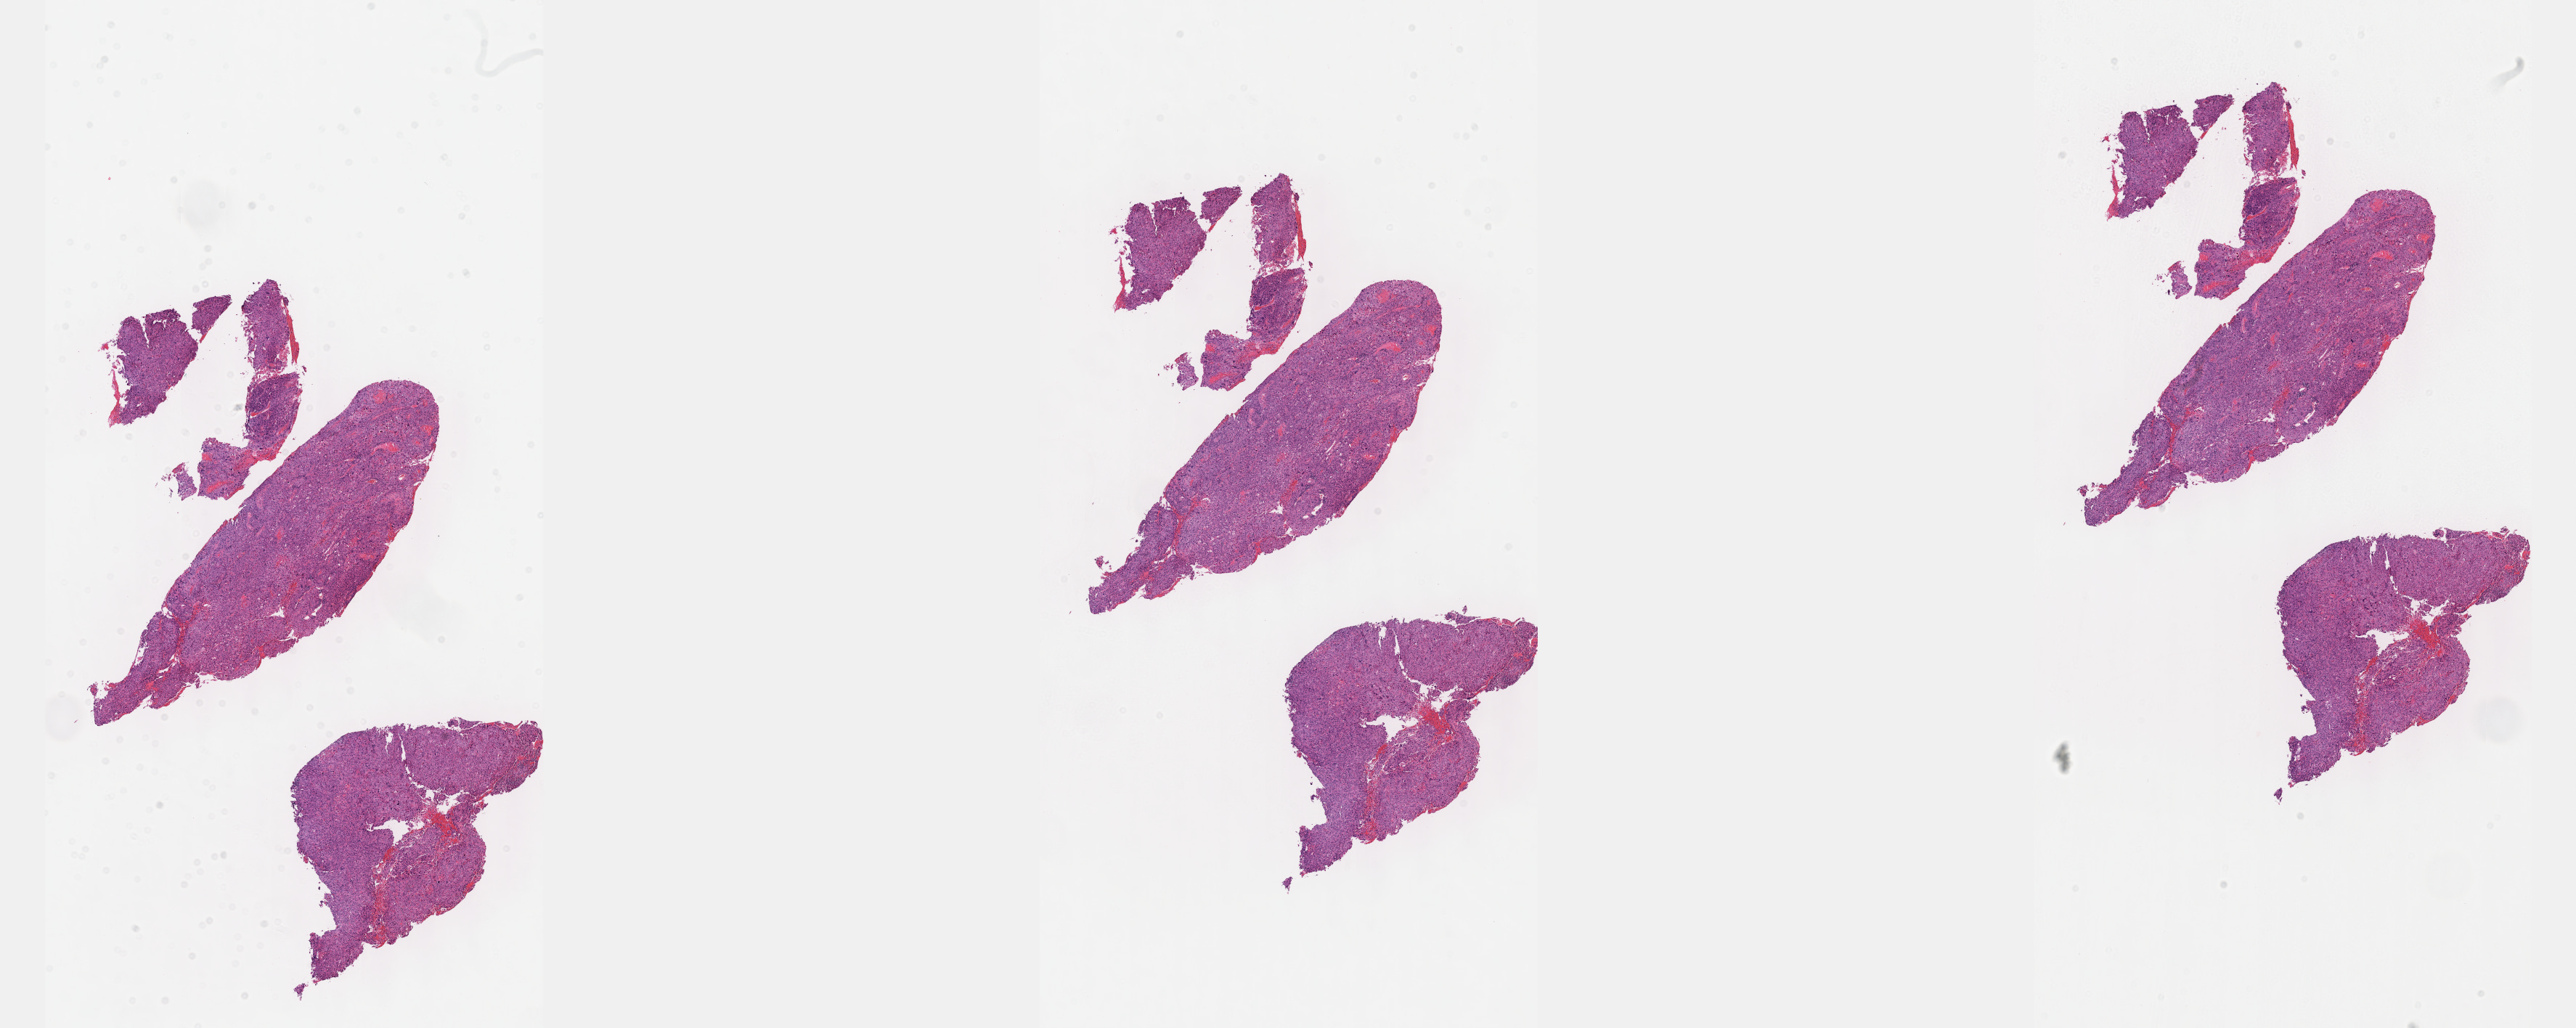
H&E whole-slide image, shown as a low-resolution overview of the whole scanned area (about 28.7 x 11.4 mm, acquisition: 40x scan); formalin-fixed paraffin-embedded (FFPE) diagnostic section; cervix, primary tumour sample. Patient: female, age at initial diagnosis 28 years. Histologic grade: G3 (poorly differentiated).
Histologic diagnosis: Squamous cell carcinoma, NOS. FIGO stage: IIA.